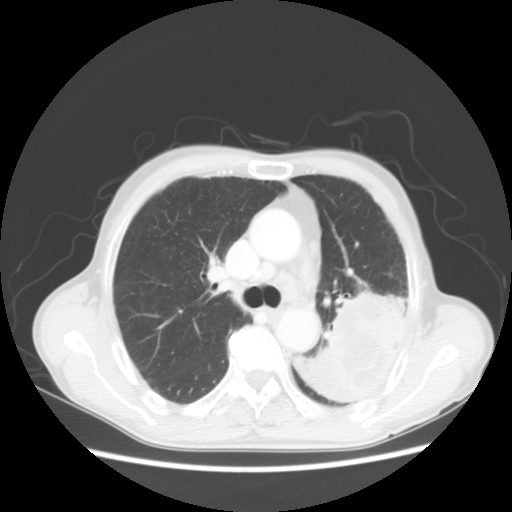
Chest CT, one axial slice; slice 34 of 51 in the series (ordered by position); reconstruction kernel STANDARD; 120 kVp; lung window (W 1500 / L -600 HU); 512 × 512 image matrix, field of view 360 × 360 mm. Patient: male, 64 years. Case-level facts recorded for this patient, not image findings: clinical TNM (as recorded): T4 N0 M0; histopathological grade: G2-3.
Annotated regions visible in this slice (bounding box drawn by a radiologist):
- lung tumour (recorded histology: squamous cell carcinoma): bounding box (x1, y1, x2, y2) in pixels: (322, 302, 409, 400)